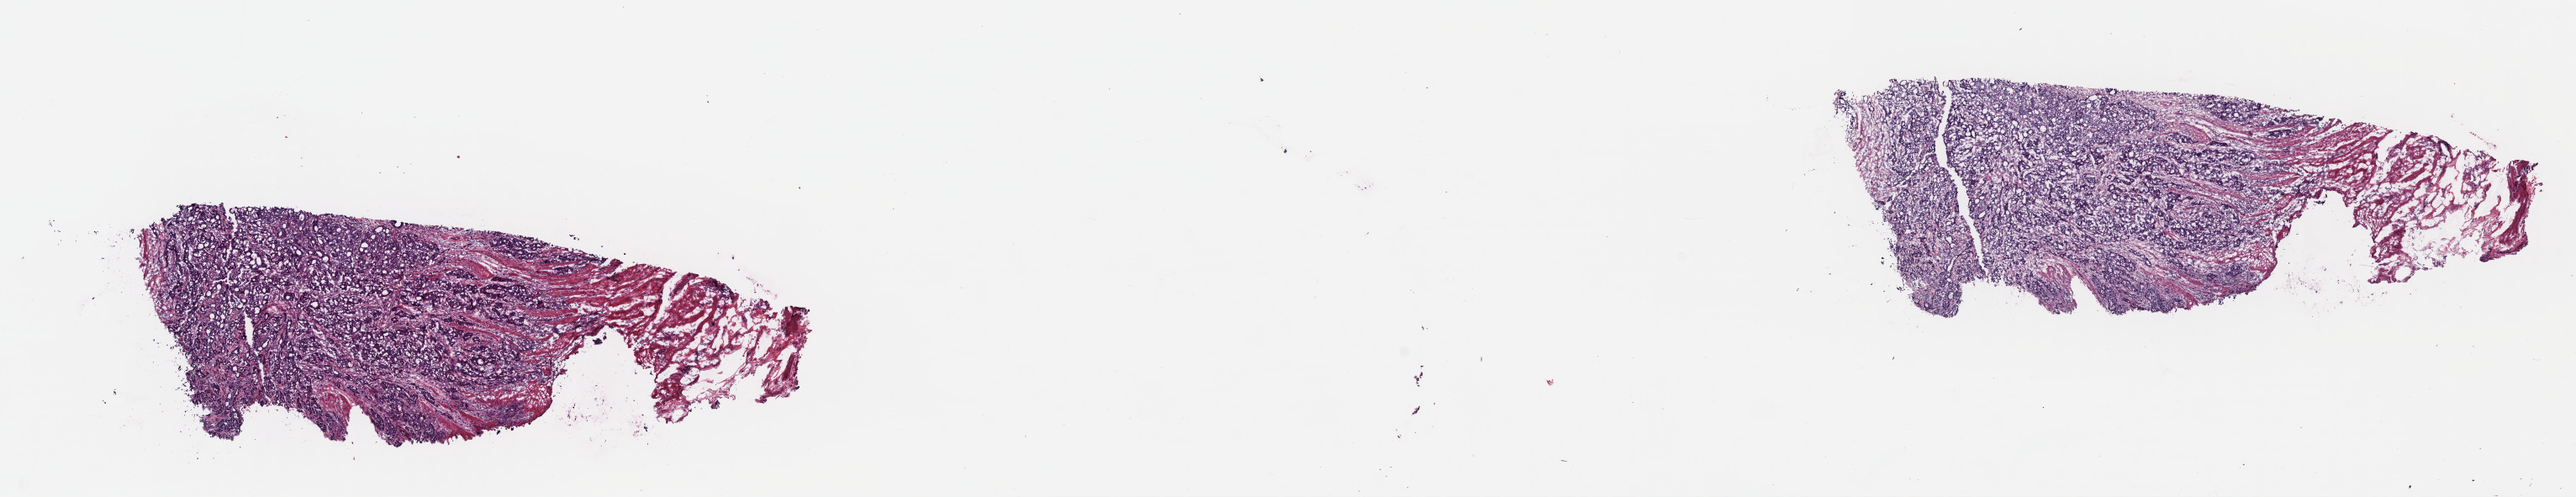
H&E-stained whole-slide image, low-resolution overview of the scanned area, about 24.1 x 4.6 mm (slide scanned at 40x); frozen section from the top of the tissue portion; primary tumour sample from the stomach. Male patient; age at initial diagnosis 57 years. Histologic grade: G2 (moderately differentiated). Pathologist review of this section (percent, as recorded): tumour cells 100%, tumour nuclei 85%, normal cells 0%, stromal cells 0%, necrosis 0%. Inflammatory infiltration, as recorded: lymphocyte infiltration 1%, monocyte infiltration 0%, neutrophil infiltration 0%.
- AJCC pathologic stage: IIA
- TNM: T3 N0 M0
- diagnosis: Adenocarcinoma, NOS (cardia, NOS)